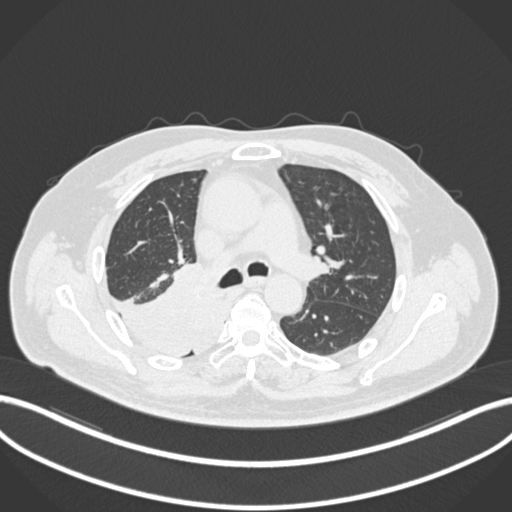
Chest CT, one axial slice; position 129 of 218 along the scan axis; reconstruction kernel B30f; lung window (W 1500 / L -600 HU); 1 mm slice thickness; 512 × 512 image matrix, field of view 400 × 400 mm. Male patient, age 68 years. From the clinical record (not read from this slice): clinical TNM (as recorded): T2a N0 M0.
Outlined on this slice (bounding box drawn by a radiologist):
- lung tumour (recorded histology: adenocarcinoma): bounding box <114,263,229,358> (left, top, right, bottom; pixels)